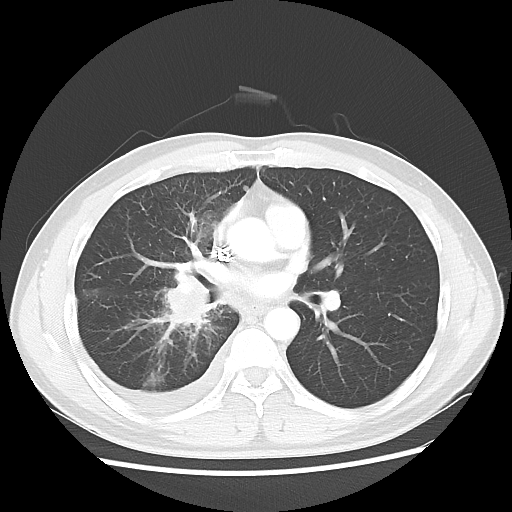
Chest CT, one axial slice. Position 28 of 56 along the scan axis. Reconstruction kernel LUNG. 120 kVp. Lung window (W 1500 / L -600 HU). 5 mm slice thickness. 512 × 512 image matrix. Male patient, age 46 years. From the clinical record (not read from this slice): clinical TNM (as recorded): T2 N3 M1.
Outlined on this slice (rectangle marked by the reading radiologist):
- lung tumour (recorded histology: adenocarcinoma): bounding box (x1, y1, x2, y2) in pixels: (154, 265, 211, 339)